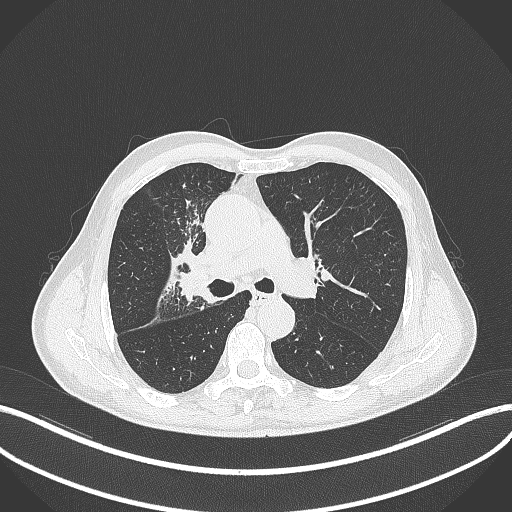
Chest CT, one axial slice. Position 305 of 490 along the scan axis. 120 kVp. Lung window (W 1500 / L -600 HU). 1 mm slice thickness. 512 × 512 image matrix. Male patient, age 69 years. Case-level facts recorded for this patient, not image findings: clinical TNM (as recorded): T2a N0 M0.
Outlined on this slice (rectangle marked by the reading radiologist):
- lung tumour (recorded histology: adenocarcinoma): box from (x=170, y=245) to (x=212, y=298) px